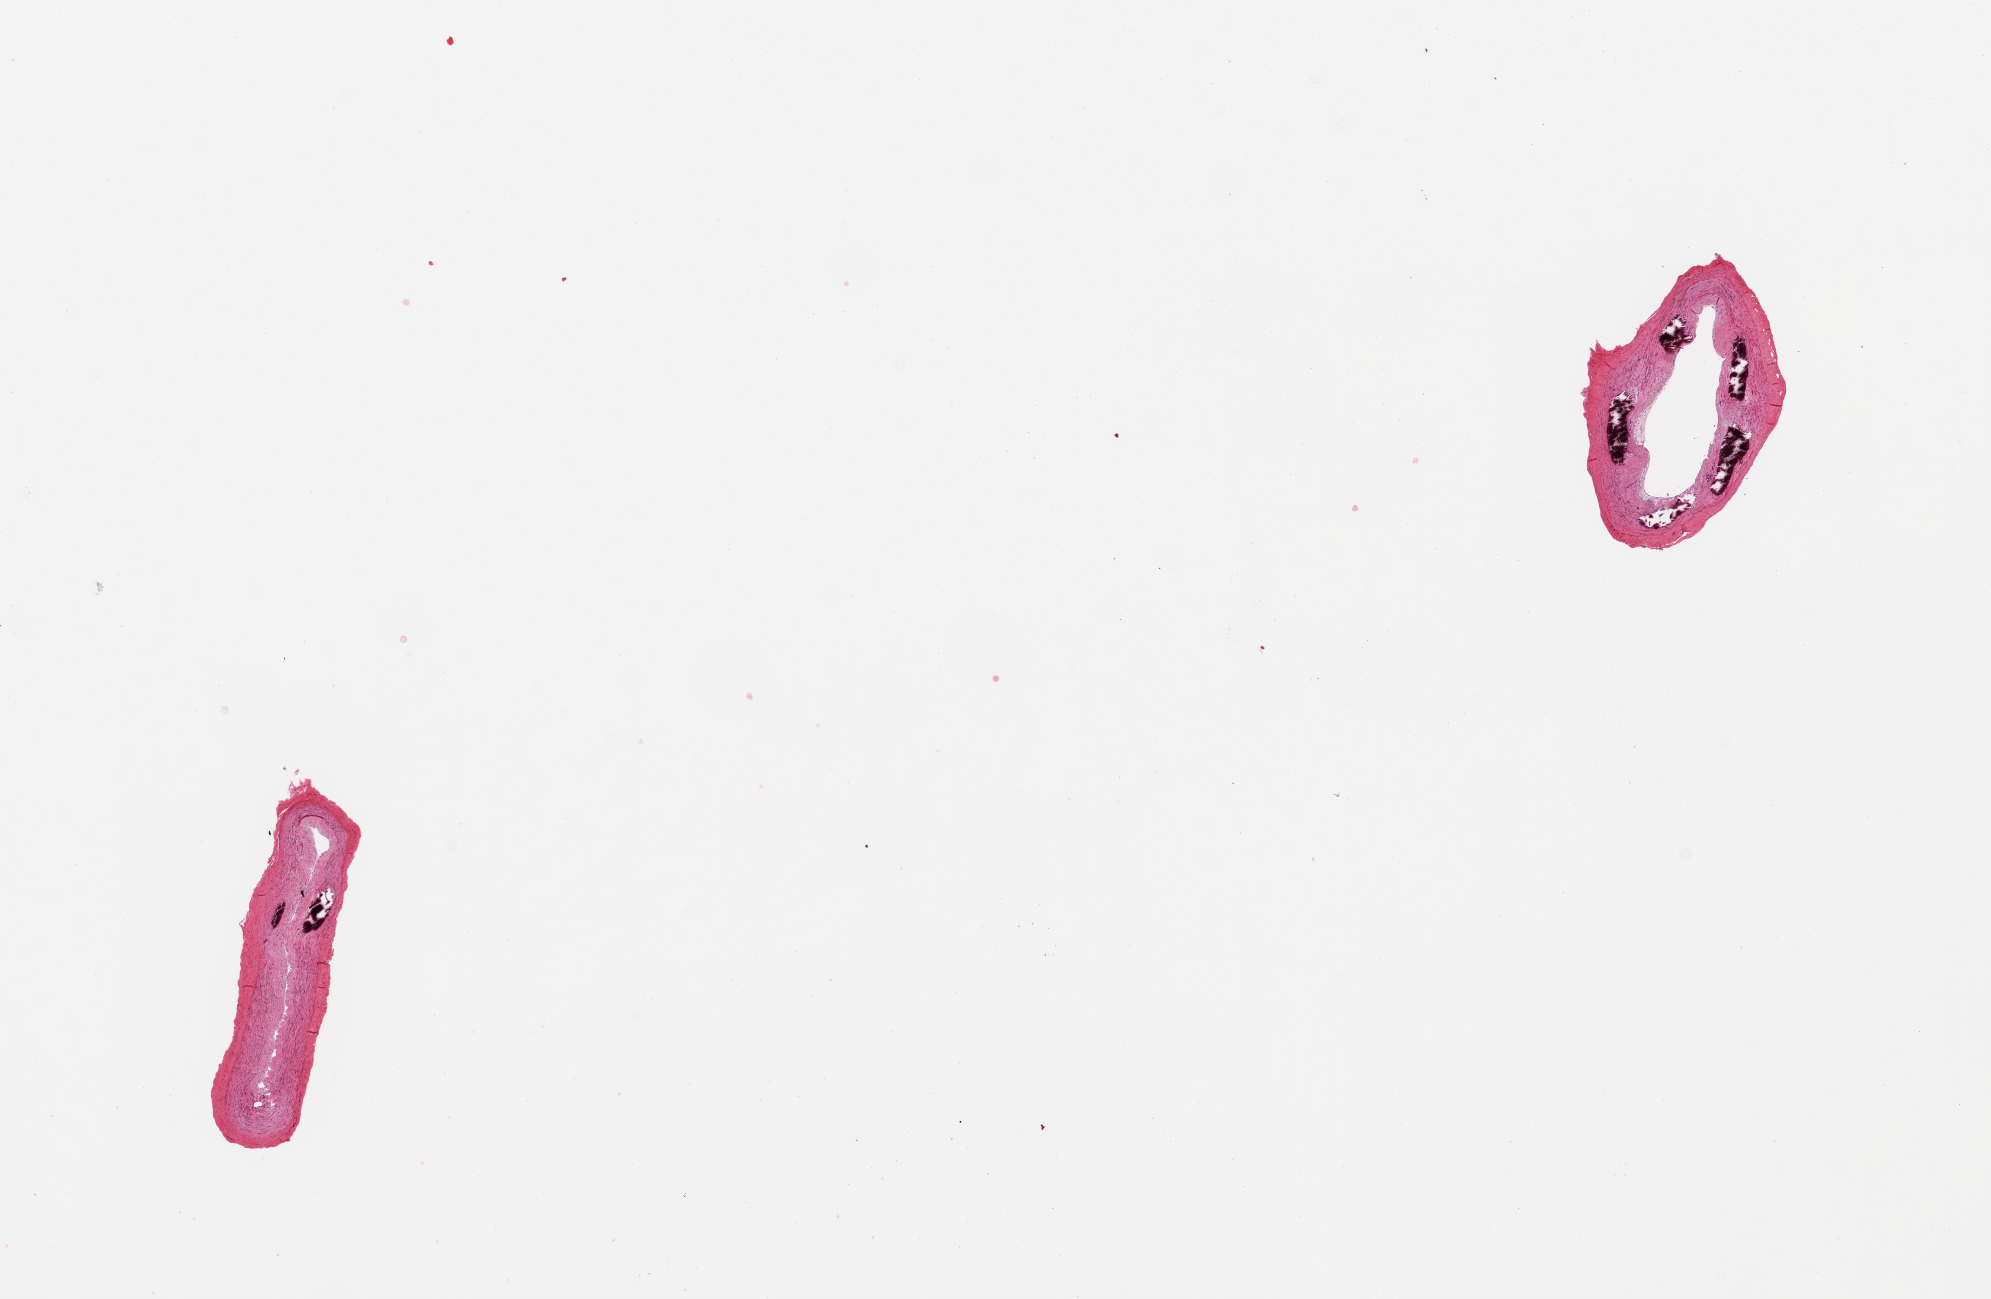
Whole-slide image, H&E stain, a low-resolution overview of the entire scanned area, about 15.8 x 10.3 mm (slide scanned at 20x); PAXgene-fixed paraffin-embedded (PFPE) section; sampled site (target tissue): tibial artery; tissue donor sample. Male donor.
Pathologist's review note for this sample: 2 pieces; 1 piece has 40% medial calcification; other has 10%; well trimmed.